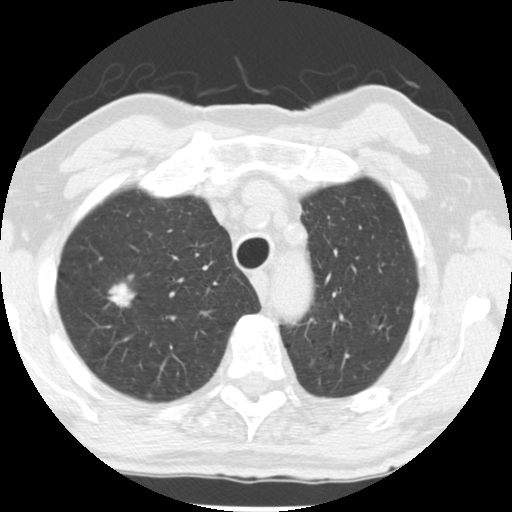
Low-dose screening chest CT, one axial slice; reconstruction kernel STANDARD; lung window (W 1500 / L -600 HU); 2.5 mm slice thickness; 512 × 512 image matrix.
Structures marked on this image (outlined manually by an expert reader):
- lesion 1 (tumor, upper lobe of right lung): bounding box (x1, y1, x2, y2) in pixels: (108, 282, 136, 308)